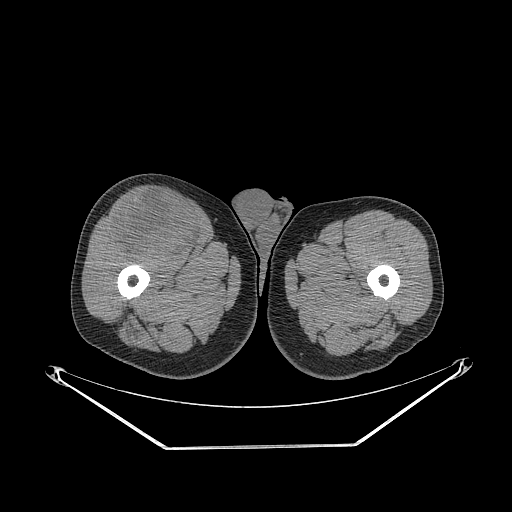
CT of an extremity soft-tissue mass (from a PET/CT study), one axial slice. Position 280 of 311 along the scan axis. 140 kVp. Soft-tissue window (W 400 / L 40 HU). 512 × 512 image matrix, field of view 500 × 500 mm. Male patient. From the clinical record (not read from this slice): histological type: pleiomorphic leiomyosarcoma; grade: intermediate; site of the primary tumour: right thigh.
Outlined on this slice (expert contour drawn on MRI and transferred to this co-registered scan by the dataset authors):
- gross tumour volume including surrounding oedema: bounding box (x1, y1, x2, y2) in pixels: (112, 192, 202, 259)
- gross tumour volume (mass): (112, 192, 202, 259)